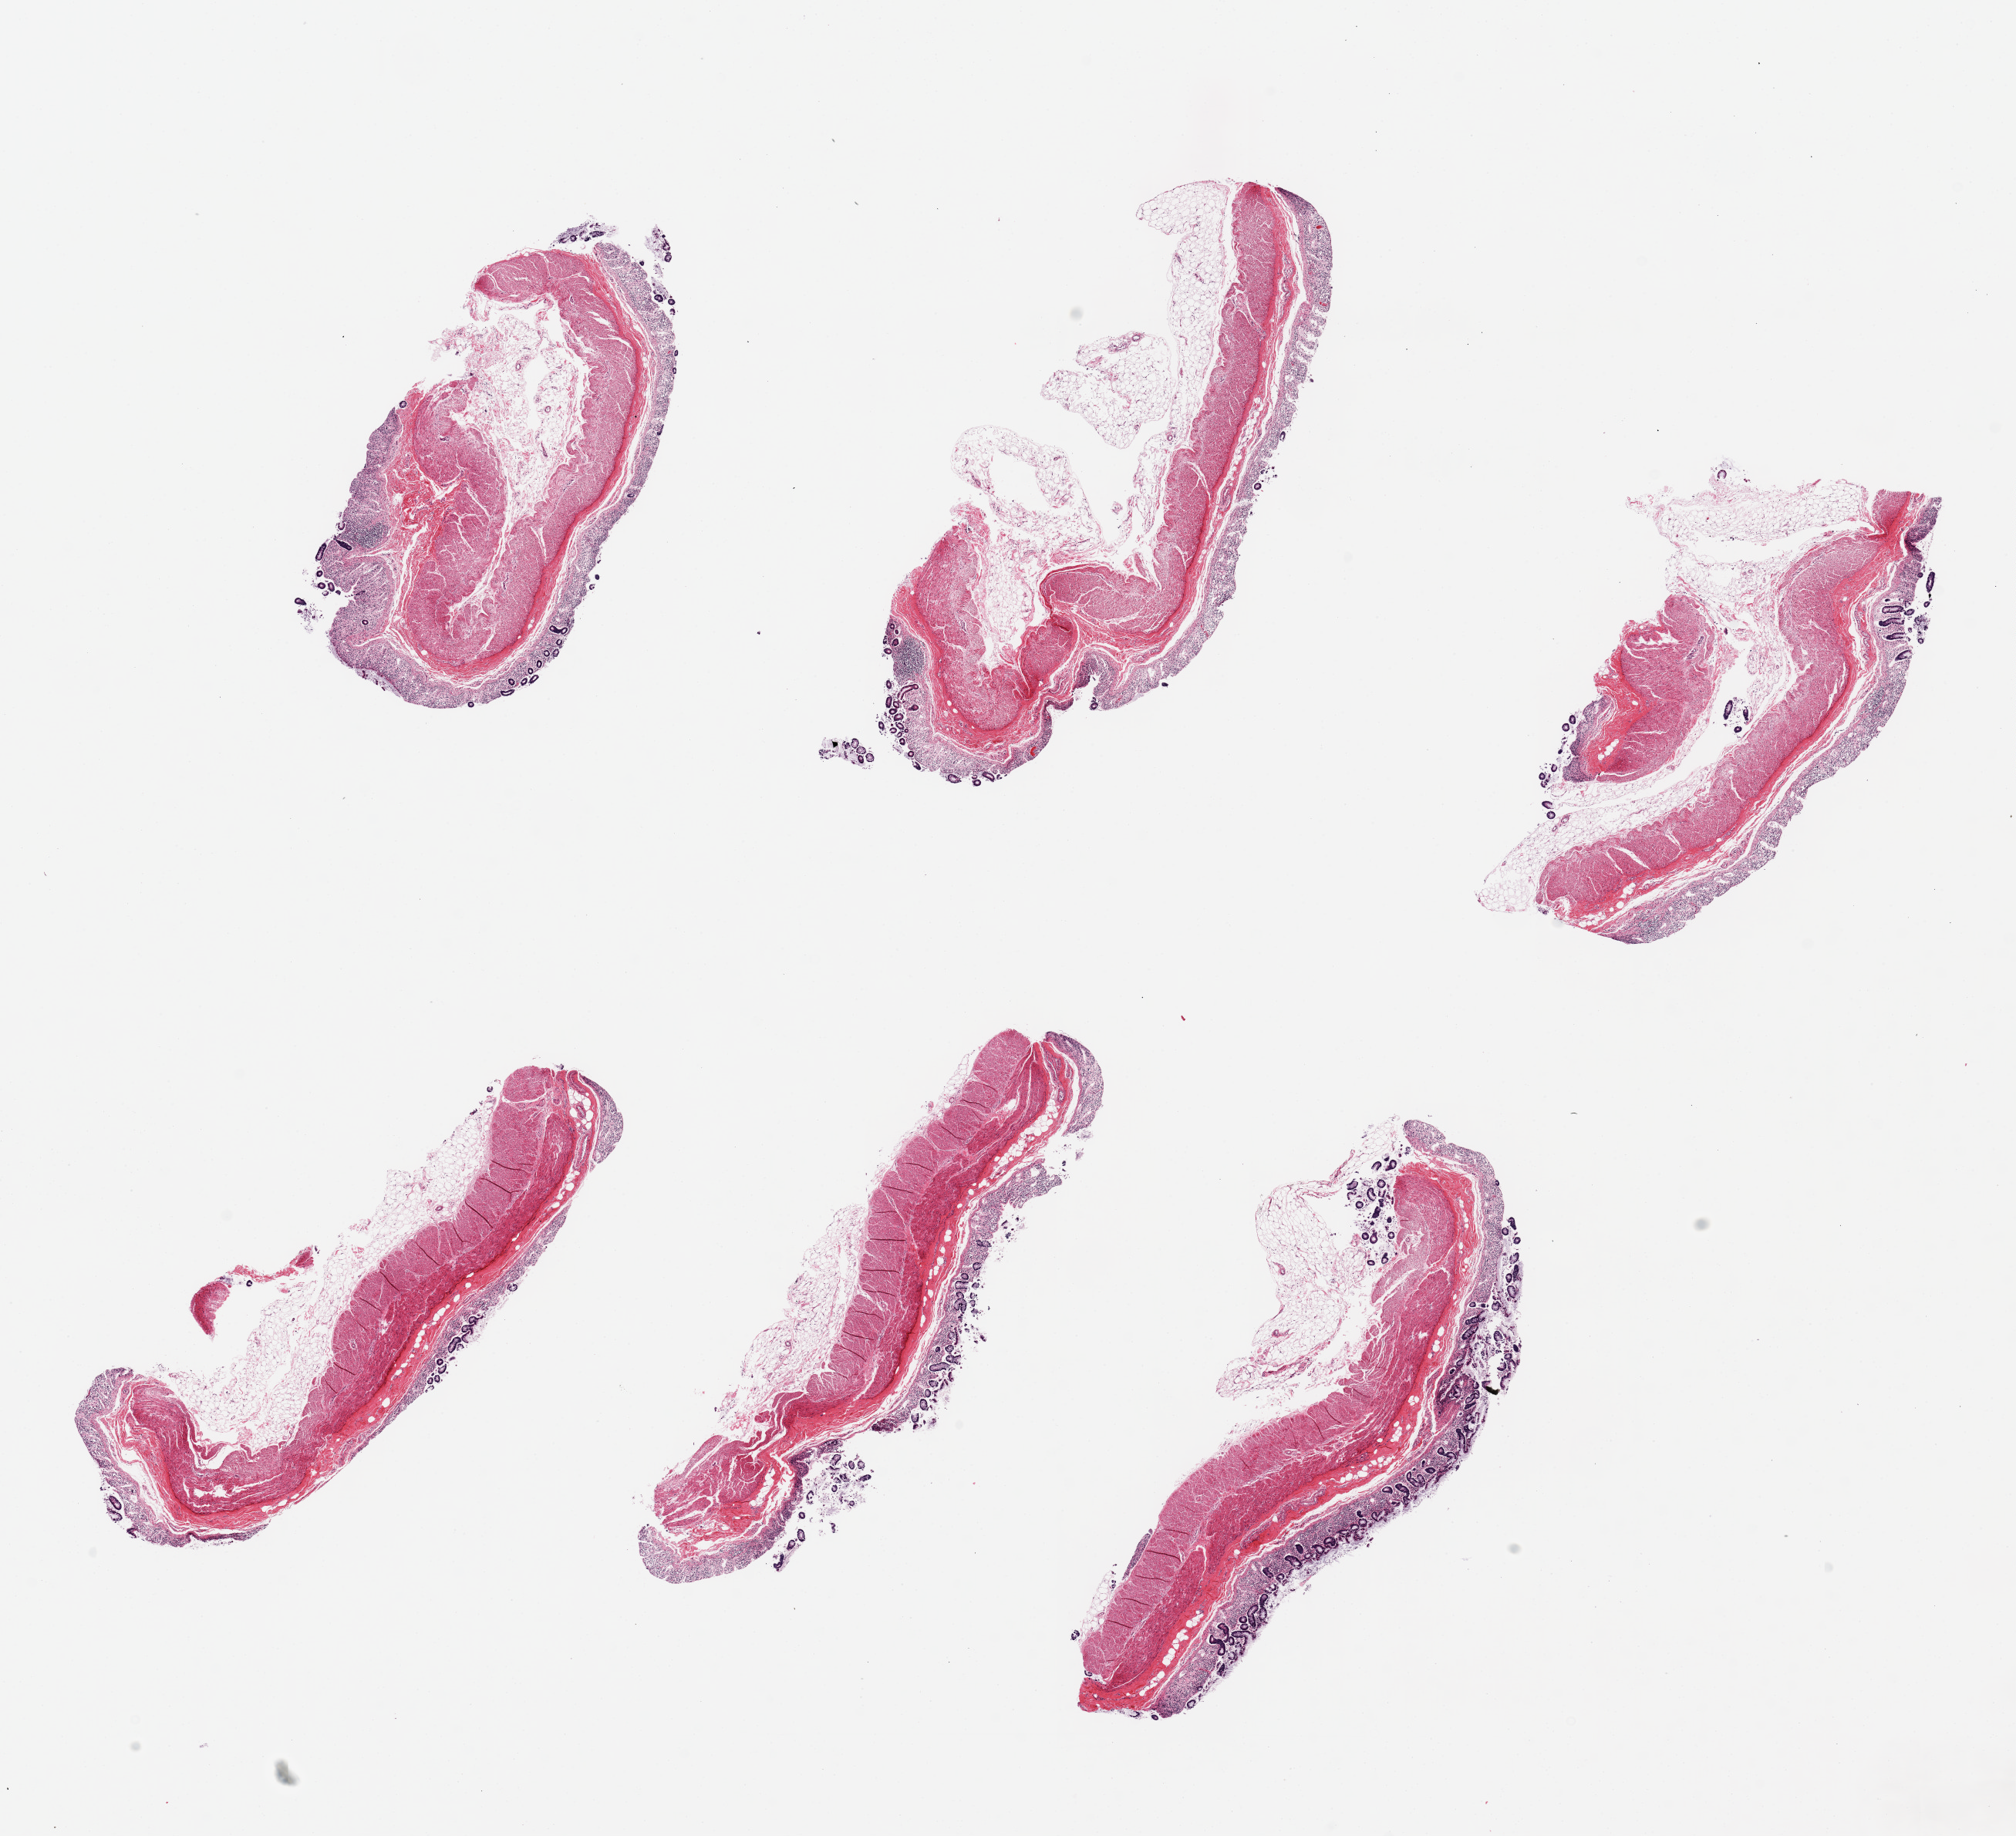
Digitized H&E-stained section, whole scanned area (about 20.7 x 18.8 mm, from a 20x scan) shown as a low-resolution overview; PAXgene-fixed, paraffin-embedded tissue; section of transverse colon (target tissue); tissue donor sample. Donor: male.
- review note (as recorded): 6 pieces, up to 7x3mm; mucosa mostly 3, some foci are 2; muscularis=2 (autolysis)